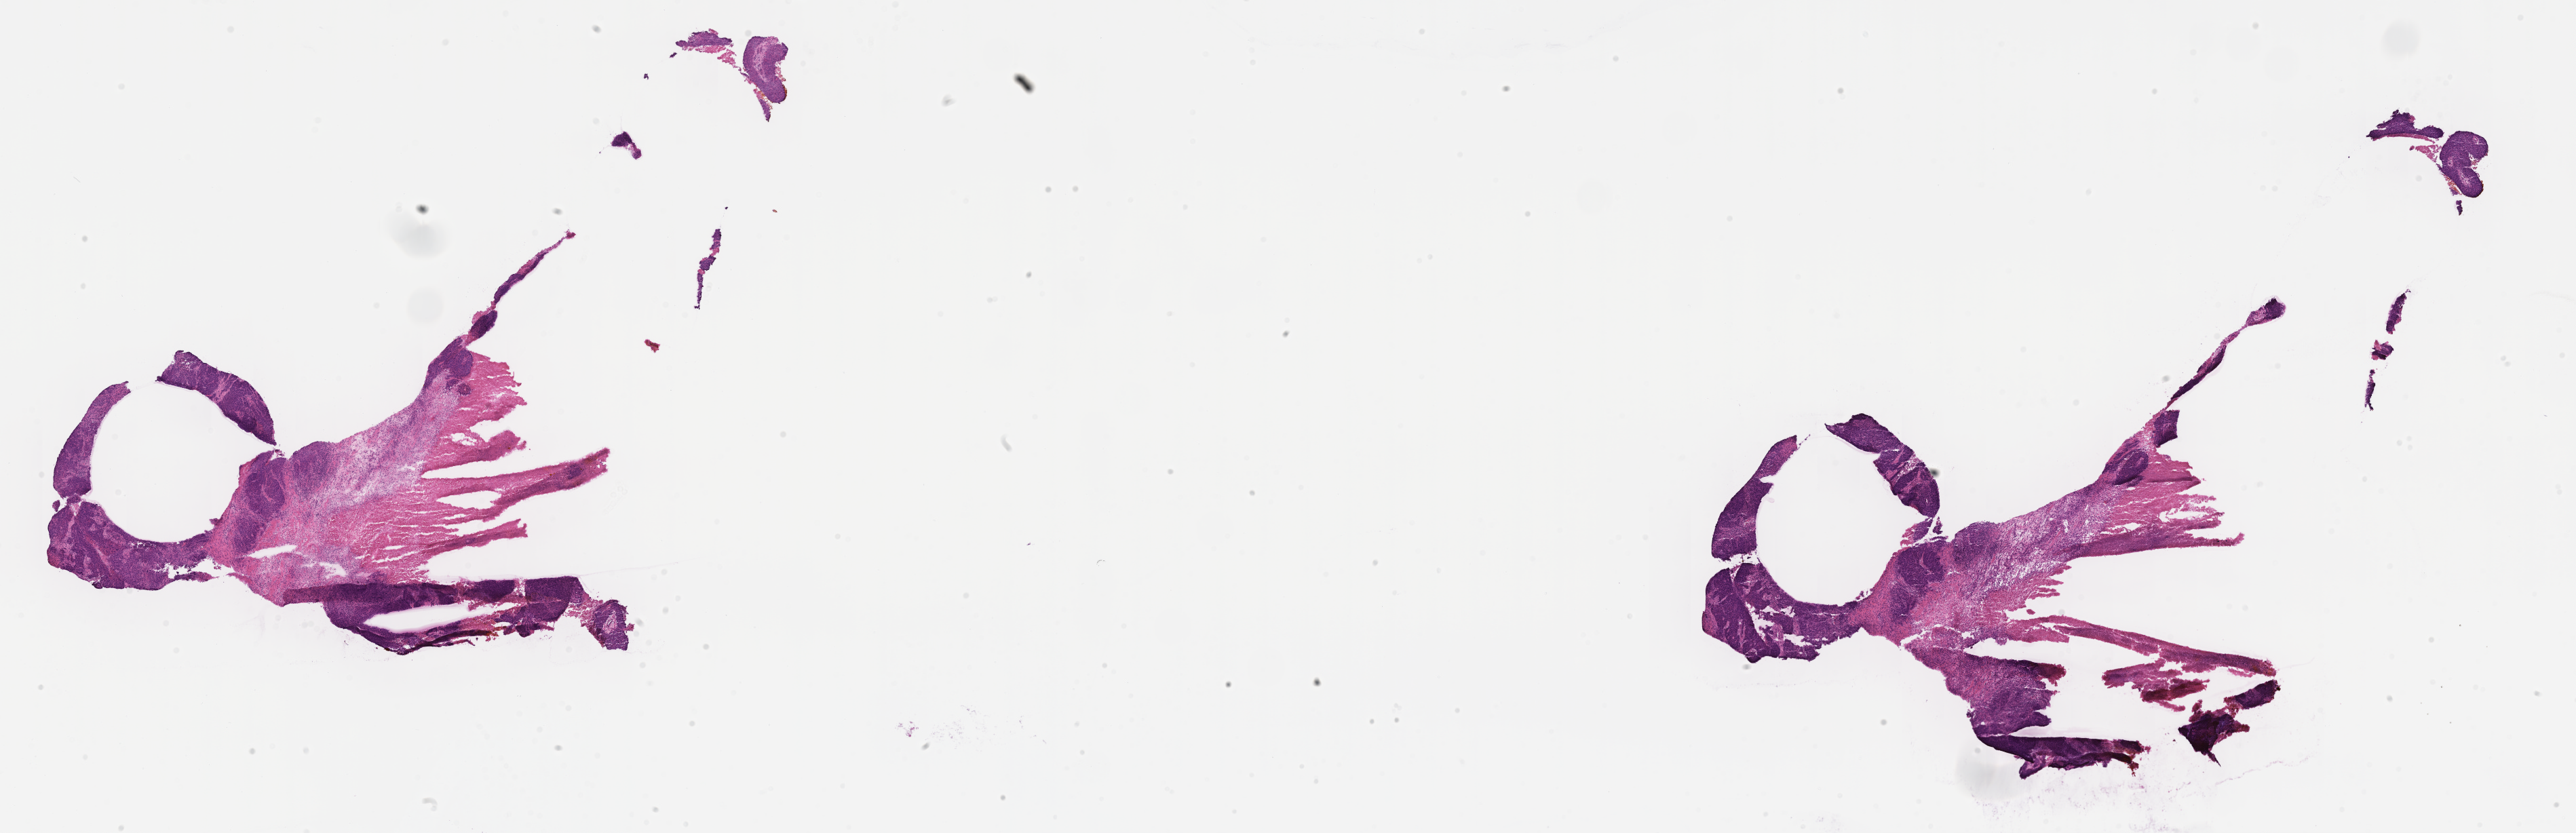
Whole-slide image, haematoxylin and eosin stain, shown as a low-resolution overview of the whole scanned area (about 30.6 x 9.9 mm). Frozen section. Specimen: primary tumor. Site: breast (right). Female patient; age at initial diagnosis 41 years. Pathologist review of this section (percent, as recorded): tumor cells 60%, tumor nuclei 60%, stromal cells 15%, necrosis 25%, normal cells 0%. Infiltration values recorded for this section: lymphocyte infiltration 3%, monocyte infiltration 2%, neutrophil infiltration 6%.
- histologic diagnosis: Infiltrating duct carcinoma, NOS